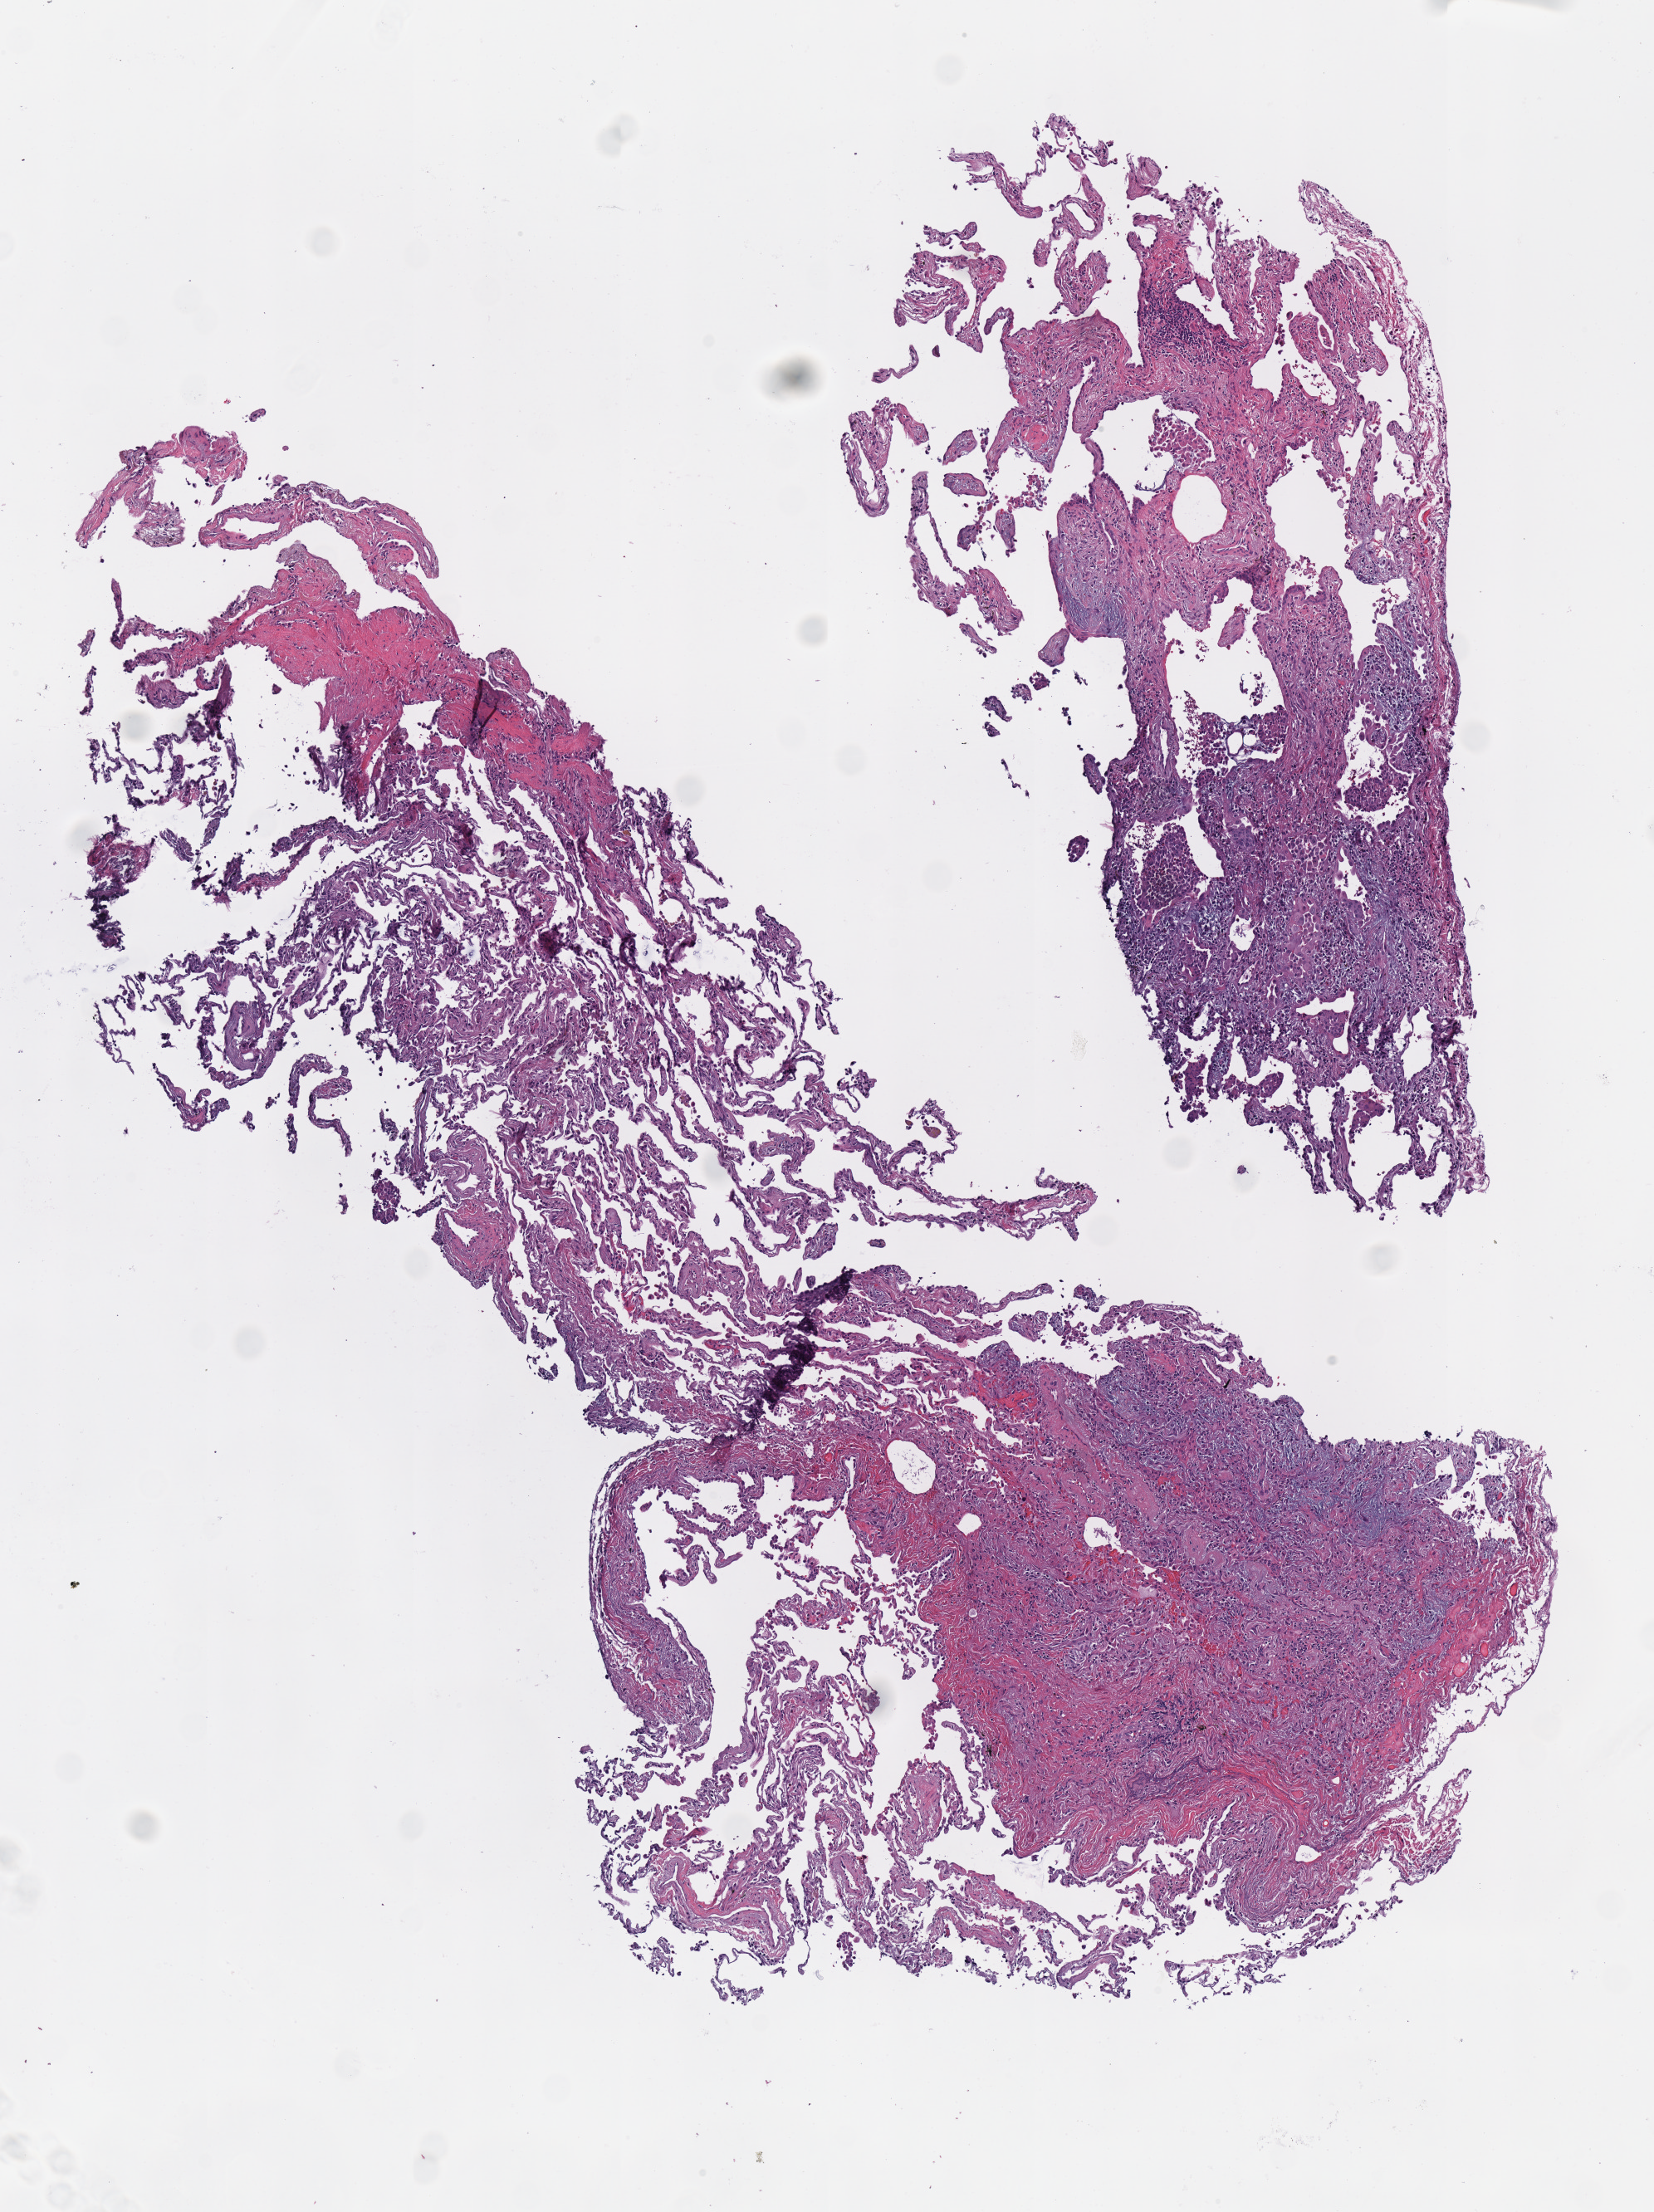
Digitized H&E tissue section (whole slide) — a low-resolution overview of the entire scanned area, about 3.9 x 5.2 mm; frozen section; sample: solid tissue normal (non-tumour tissue), lung. Male, age 70 years at initial diagnosis.
This section: solid tissue normal (non-tumour) sample from the same patient. Patient diagnosis: Squamous cell carcinoma, NOS.